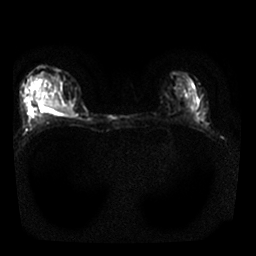
Breast MRI, one axial slice; slice 14 of 25 in the series (ordered by position); diffusion-weighted series; image 2 of 4 stored at this slice position (different b-values; order by instance number); 1.5 T; 4 mm slice thickness; 256 × 256 image matrix. Female patient.
Outlined on this slice (outlined manually by an expert reader):
- tumour on diffusion-weighted imaging: bounding box <34,92,71,115> (left, top, right, bottom; pixels)